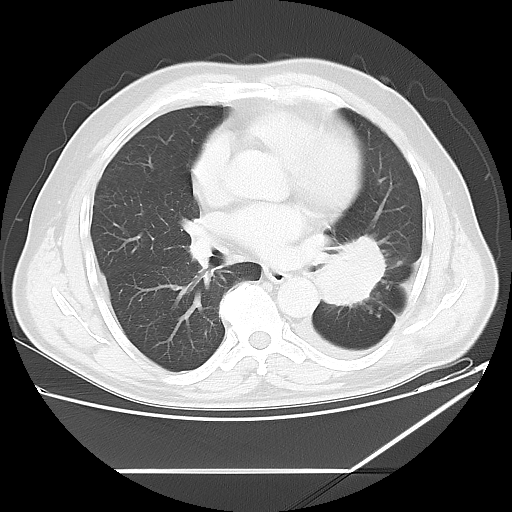
Chest CT, one axial slice; position 30 of 60 along the scan axis; reconstruction kernel LUNG; 120 kVp; lung window (W 1500 / L -600 HU); 5 mm slice thickness; 512 × 512 image matrix, field of view 395 × 395 mm. Male patient, age 62 years. Case-level facts recorded for this patient, not image findings: clinical TNM (as recorded): T3 N0 M1.
Annotated regions visible in this slice (bounding box drawn by a radiologist):
- lung tumour (recorded histology: adenocarcinoma): bounding box (x1, y1, x2, y2) in pixels: (316, 233, 385, 313)
- lung tumour (recorded histology: adenocarcinoma): (318, 233, 388, 312)